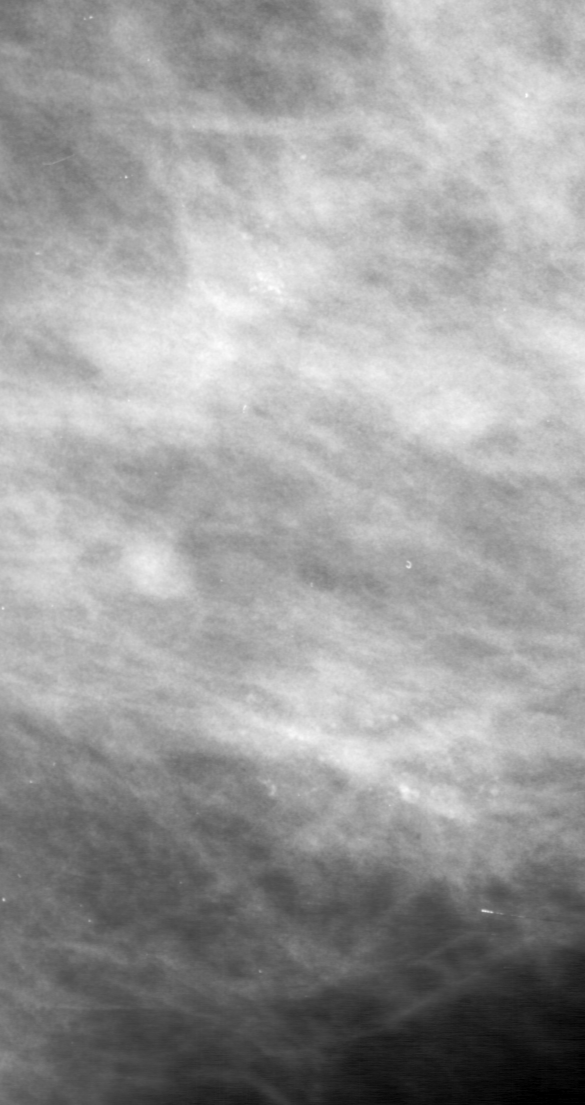
Crop from a digitized film mammogram around one marked abnormality; left breast; MLO view; BI-RADS breast density category 3 (scale 1–4).
Finding: calcifications, morphology pleomorphic, distribution clustered; BI-RADS assessment category 0 (incomplete: needs additional imaging); pathology (as recorded): malignant.